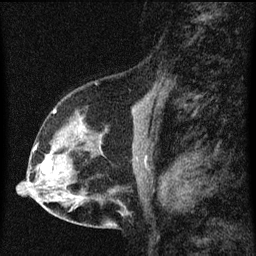
Breast MRI (dynamic contrast-enhanced), one sagittal slice. Position 37 of 60 along the scan axis. Dynamic contrast-enhanced series, image 2 of 3 at this slice position (ordered by acquisition). 1.5 T. TE 4.2 ms, TR 8 ms. 2 mm slice thickness. 256 × 256 image matrix, field of view 180 × 180 mm. Patient: female, 56 years.
Annotated regions visible in this slice (semi-automatic segmentation, software-assisted and operator-edited):
- analysis volume of interest (the breast-tissue region the enhancement analysis was run in; not a lesion): bounding box [x1, y1, x2, y2] px = [34, 114, 102, 181]
- tumour enhancement mask (voxels above the 70 % enhancement threshold inside the analysis volume of interest): [34, 147, 49, 174]